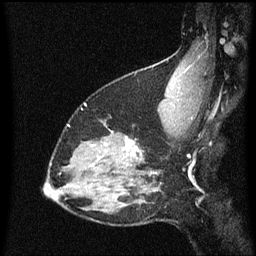
Breast MRI (dynamic contrast-enhanced), one sagittal slice; slice 46 of 60 in the series (ordered by position); dynamic contrast-enhanced series, image 2 of 3 at this slice position (ordered by acquisition); 1.5 T; TE 4.2 ms, TR 8.4 ms; 256 × 256 image matrix, field of view 200 × 200 mm. Female patient, age 38 years. Case-level facts recorded for this patient, not image findings: setting: breast cancer imaged before/during neoadjuvant chemotherapy; receptor status: HR-positive, HER2-negative.
Annotated regions visible in this slice (semi-automatically segmented with operator editing):
- analysis volume of interest (the breast-tissue region the enhancement analysis was run in; not a lesion): bounding box (x1, y1, x2, y2) in pixels: (122, 134, 145, 163)
- tumour enhancement mask (voxels above the 70 % enhancement threshold inside the analysis volume of interest): (125, 136, 143, 157)